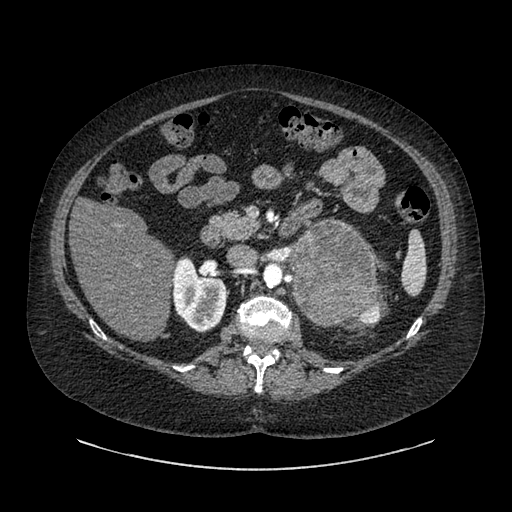
Contrast-enhanced abdominal CT, one axial slice; 120 kVp; intravenous contrast given; soft-tissue window (W 400 / L 40 HU); 0.62 mm slice thickness; 512 × 512 image matrix, field of view 460 × 460 mm. Patient: female, 61 years. From the clinical record (not read from this slice): diagnosis: adrenocortical carcinoma; tumour side: left adrenal.
Structures marked on this image (semi-automatically segmented with operator editing):
- mass: box from (x=293, y=222) to (x=375, y=326) px